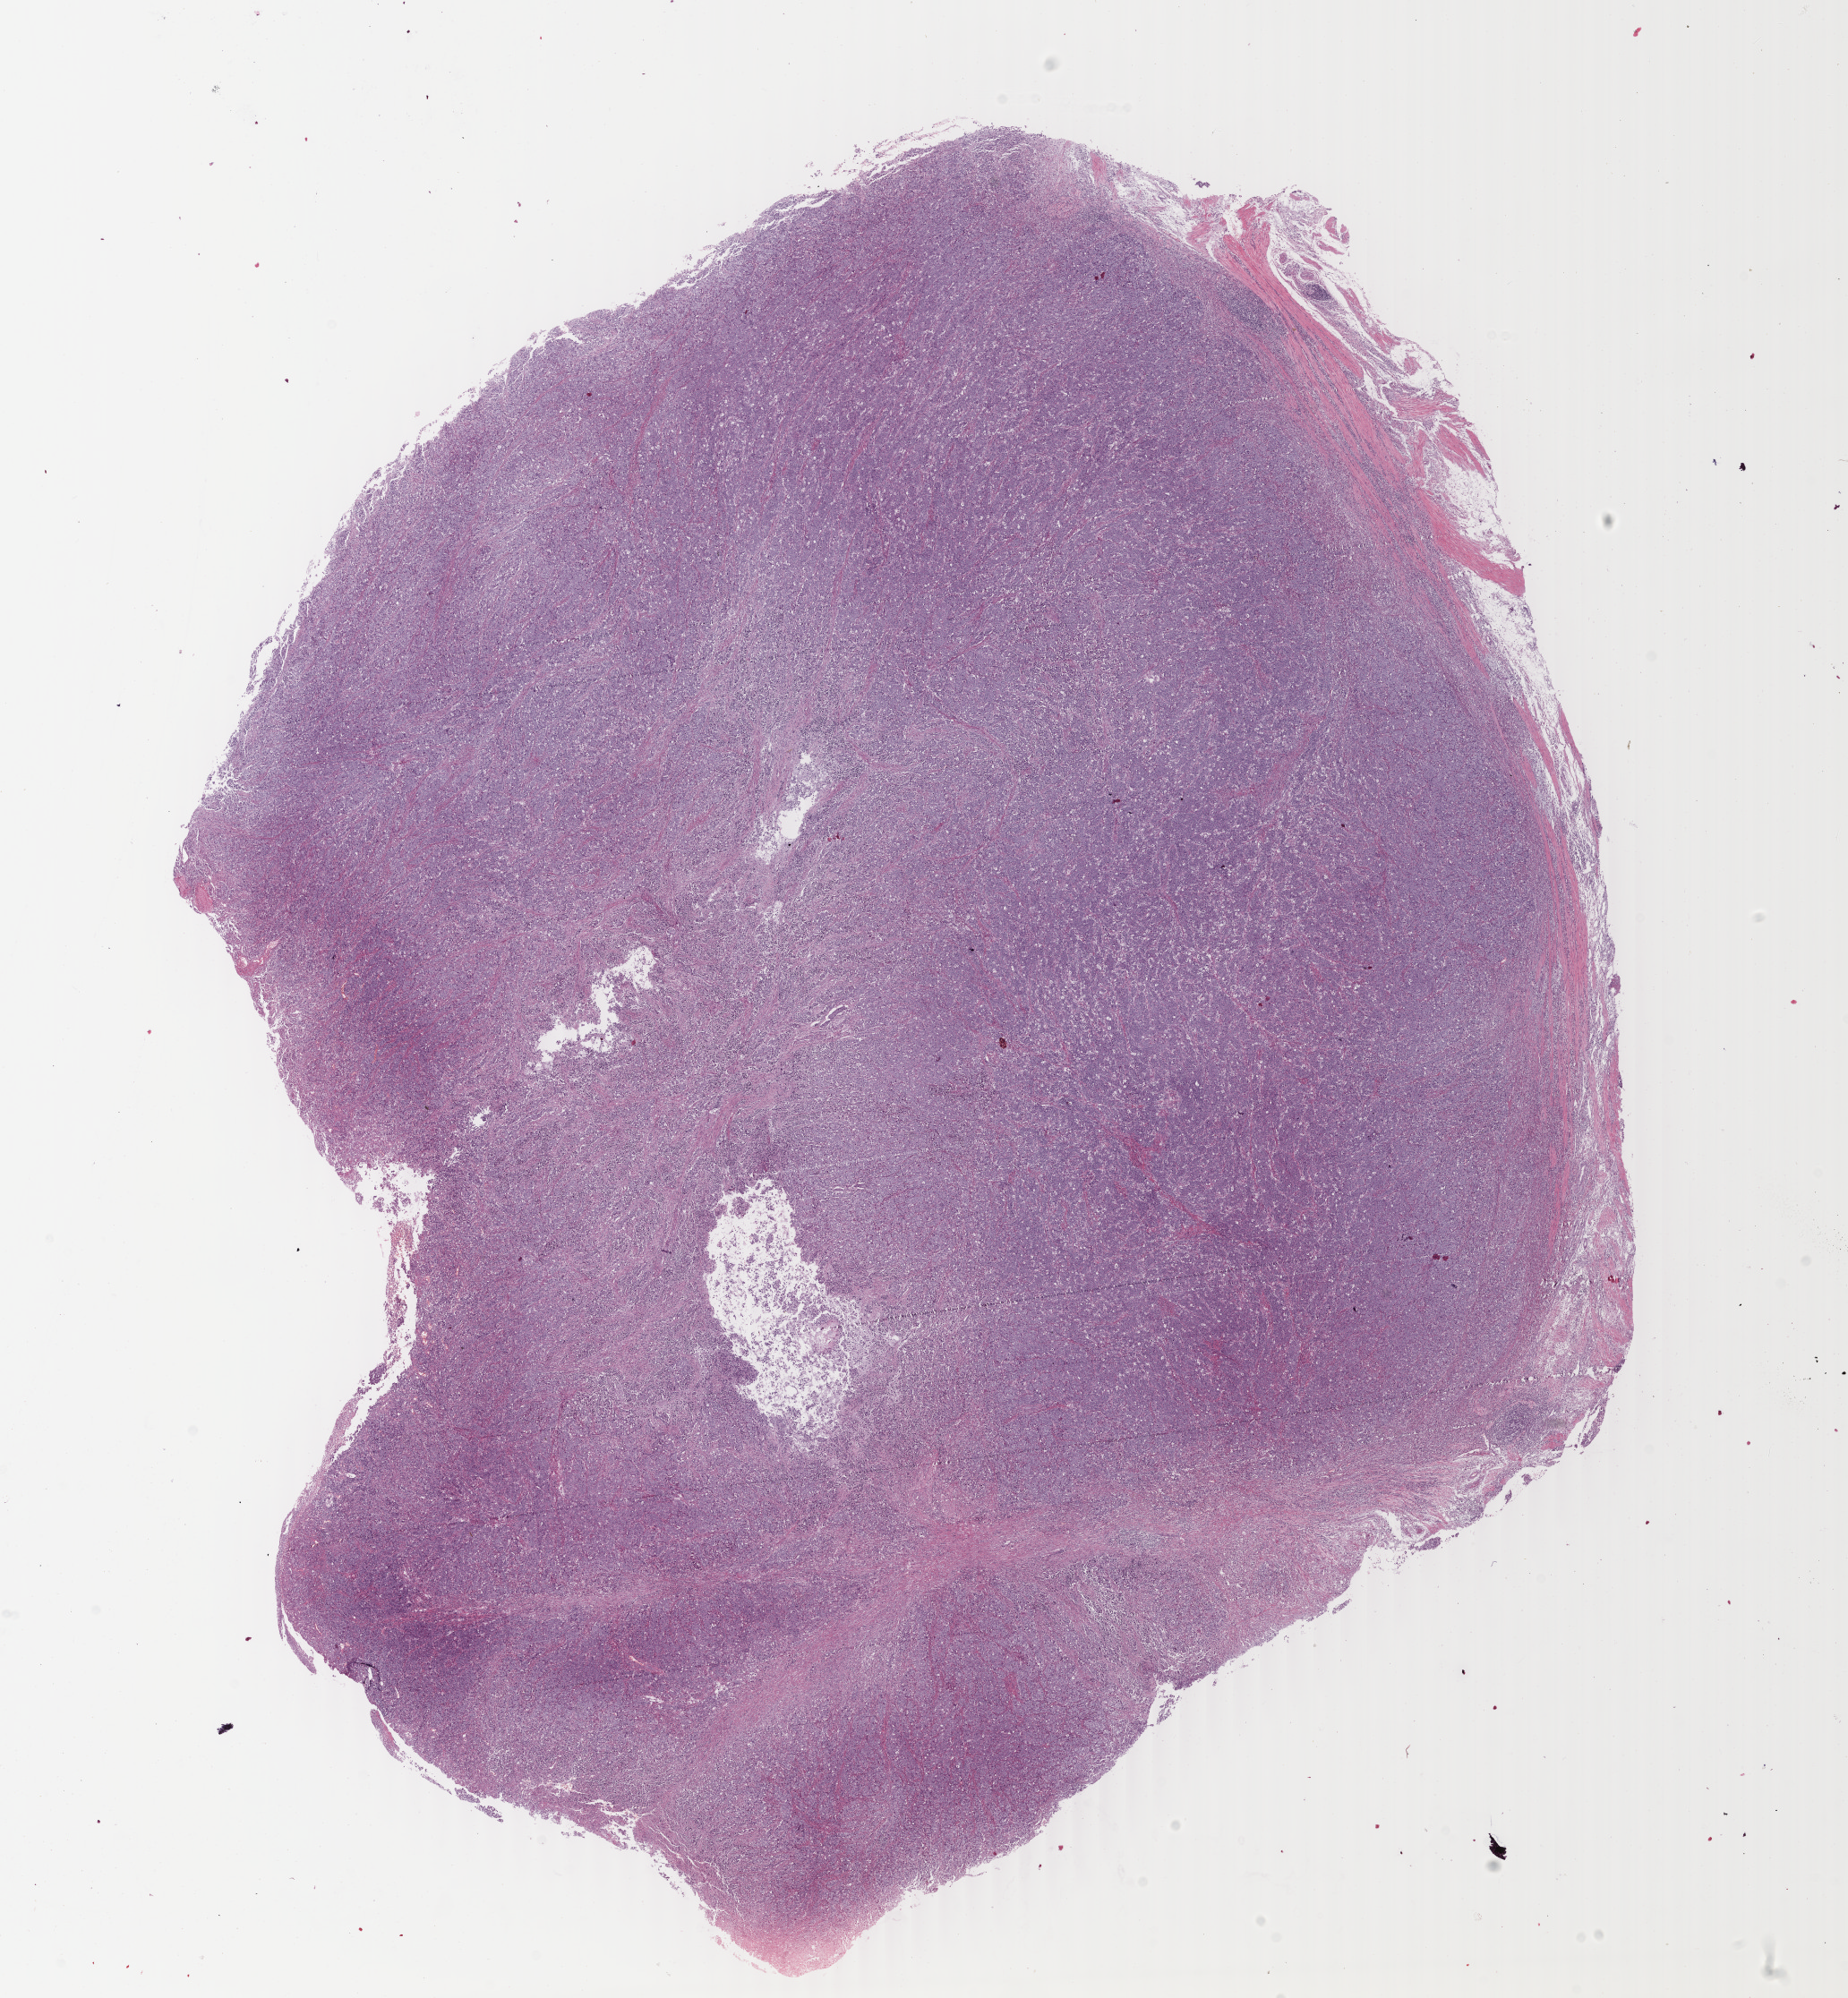
H&E-stained whole-slide image, a low-resolution overview of the entire scanned area, about 16.4 x 17.8 mm, formalin-fixed paraffin-embedded (FFPE) diagnostic section, stomach, primary tumour sample. Female patient; age at initial diagnosis 43 years. Histologic grade: G3 (poorly differentiated).
Histologic diagnosis: Adenocarcinoma, NOS (gastric antrum). AJCC pathologic stage: IIIA (6th edition).